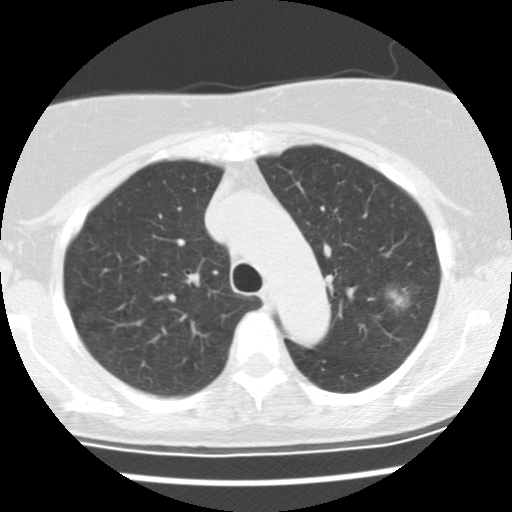
Axial slice from a low-dose chest CT screening exam, first (baseline) screen, lung window (W 1500 / L -600 HU), standard (soft-tissue) reconstruction kernel (STANDARD), slice 103 of 137 in the series. Female participant, aged 66 years at enrolment.
- Lesion marked by an expert reader, bounding box (x1, y1, x2, y2) in pixels: (376, 278, 428, 325).
- Reader record for this screening exam (exam-level; its link to the box is not recorded): non-calcified nodule or mass ≥4 mm, left upper lobe, 25 × 17 mm, poorly defined margins, mixed attenuation.
- Participant outcome: lung cancer diagnosed 44 days after this screen — bronchiolo-alveolar adenocarcinoma, NOS, left upper lobe, well differentiated (G1), stage IA (AJCC 6th edition), 19 mm at pathology.